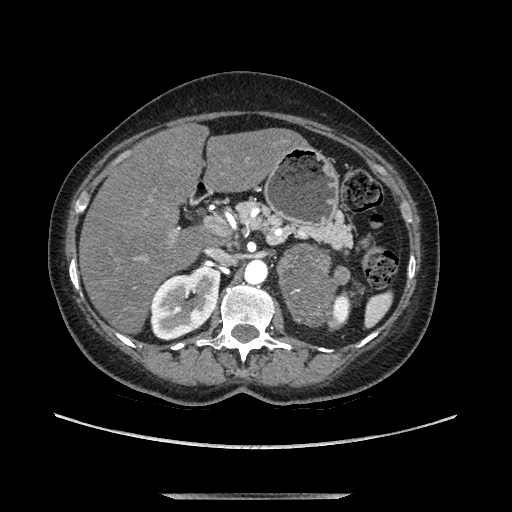
Contrast-enhanced abdominal CT, one axial slice; slice 70 of 169 in the series (ordered by position); soft-tissue window (W 400 / L 40 HU); 1.25 mm slice thickness; 512 × 512 image matrix, field of view 400 × 400 mm. Female patient. From the clinical record (not read from this slice): diagnosis: adrenocortical carcinoma; tumour side: left adrenal; tumour size at pathology: 9 cm; Ki-67 index: 2 %; stage (as recorded): 3.
Structures marked on this image (semi-automatic segmentation, software-assisted and operator-edited):
- mass: box from (x=282, y=245) to (x=336, y=326) px